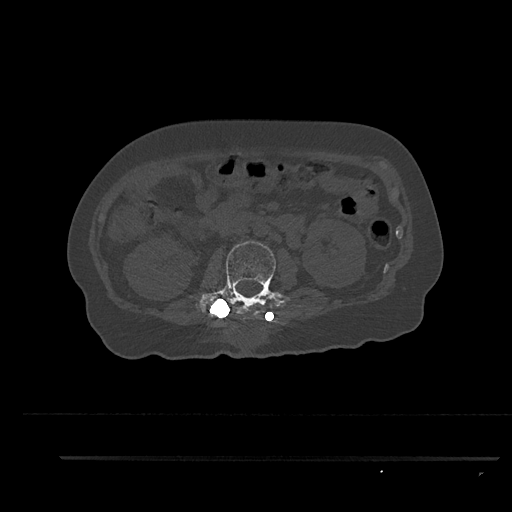
CT including the spine, one axial slice; position 154 of 797 along the scan axis; bone window (W 1800 / L 400 HU); 512 × 512 image matrix, field of view 408 × 408 mm. Patient: female, 44 years. From the clinical record (not read from this slice): primary cancer: renal.
Structures marked on this image (semi-automatic segmentation, software-assisted and operator-edited):
- L2 vertebra: box from (x=195, y=241) to (x=284, y=319) px